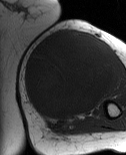
MRI of an extremity soft-tissue mass, one axial slice; slice 34 of 86 in the series (ordered by position); MR volume resampled by the dataset authors to the PET/CT grid (not the native acquisition matrix); 3.27 mm slice thickness; 126 × 155 image matrix. Female patient. Case-level facts recorded for this patient, not image findings: histological type: pleiomorphic leiomyosarcoma; grade: high; site of the primary tumour: left biceps.
Outlined on this slice (expert contour drawn on MRI and transferred to this co-registered scan by the dataset authors):
- gross tumour volume including surrounding oedema: bounding box <24,29,114,121> (left, top, right, bottom; pixels)
- gross tumour volume (mass): <24,31,114,119>